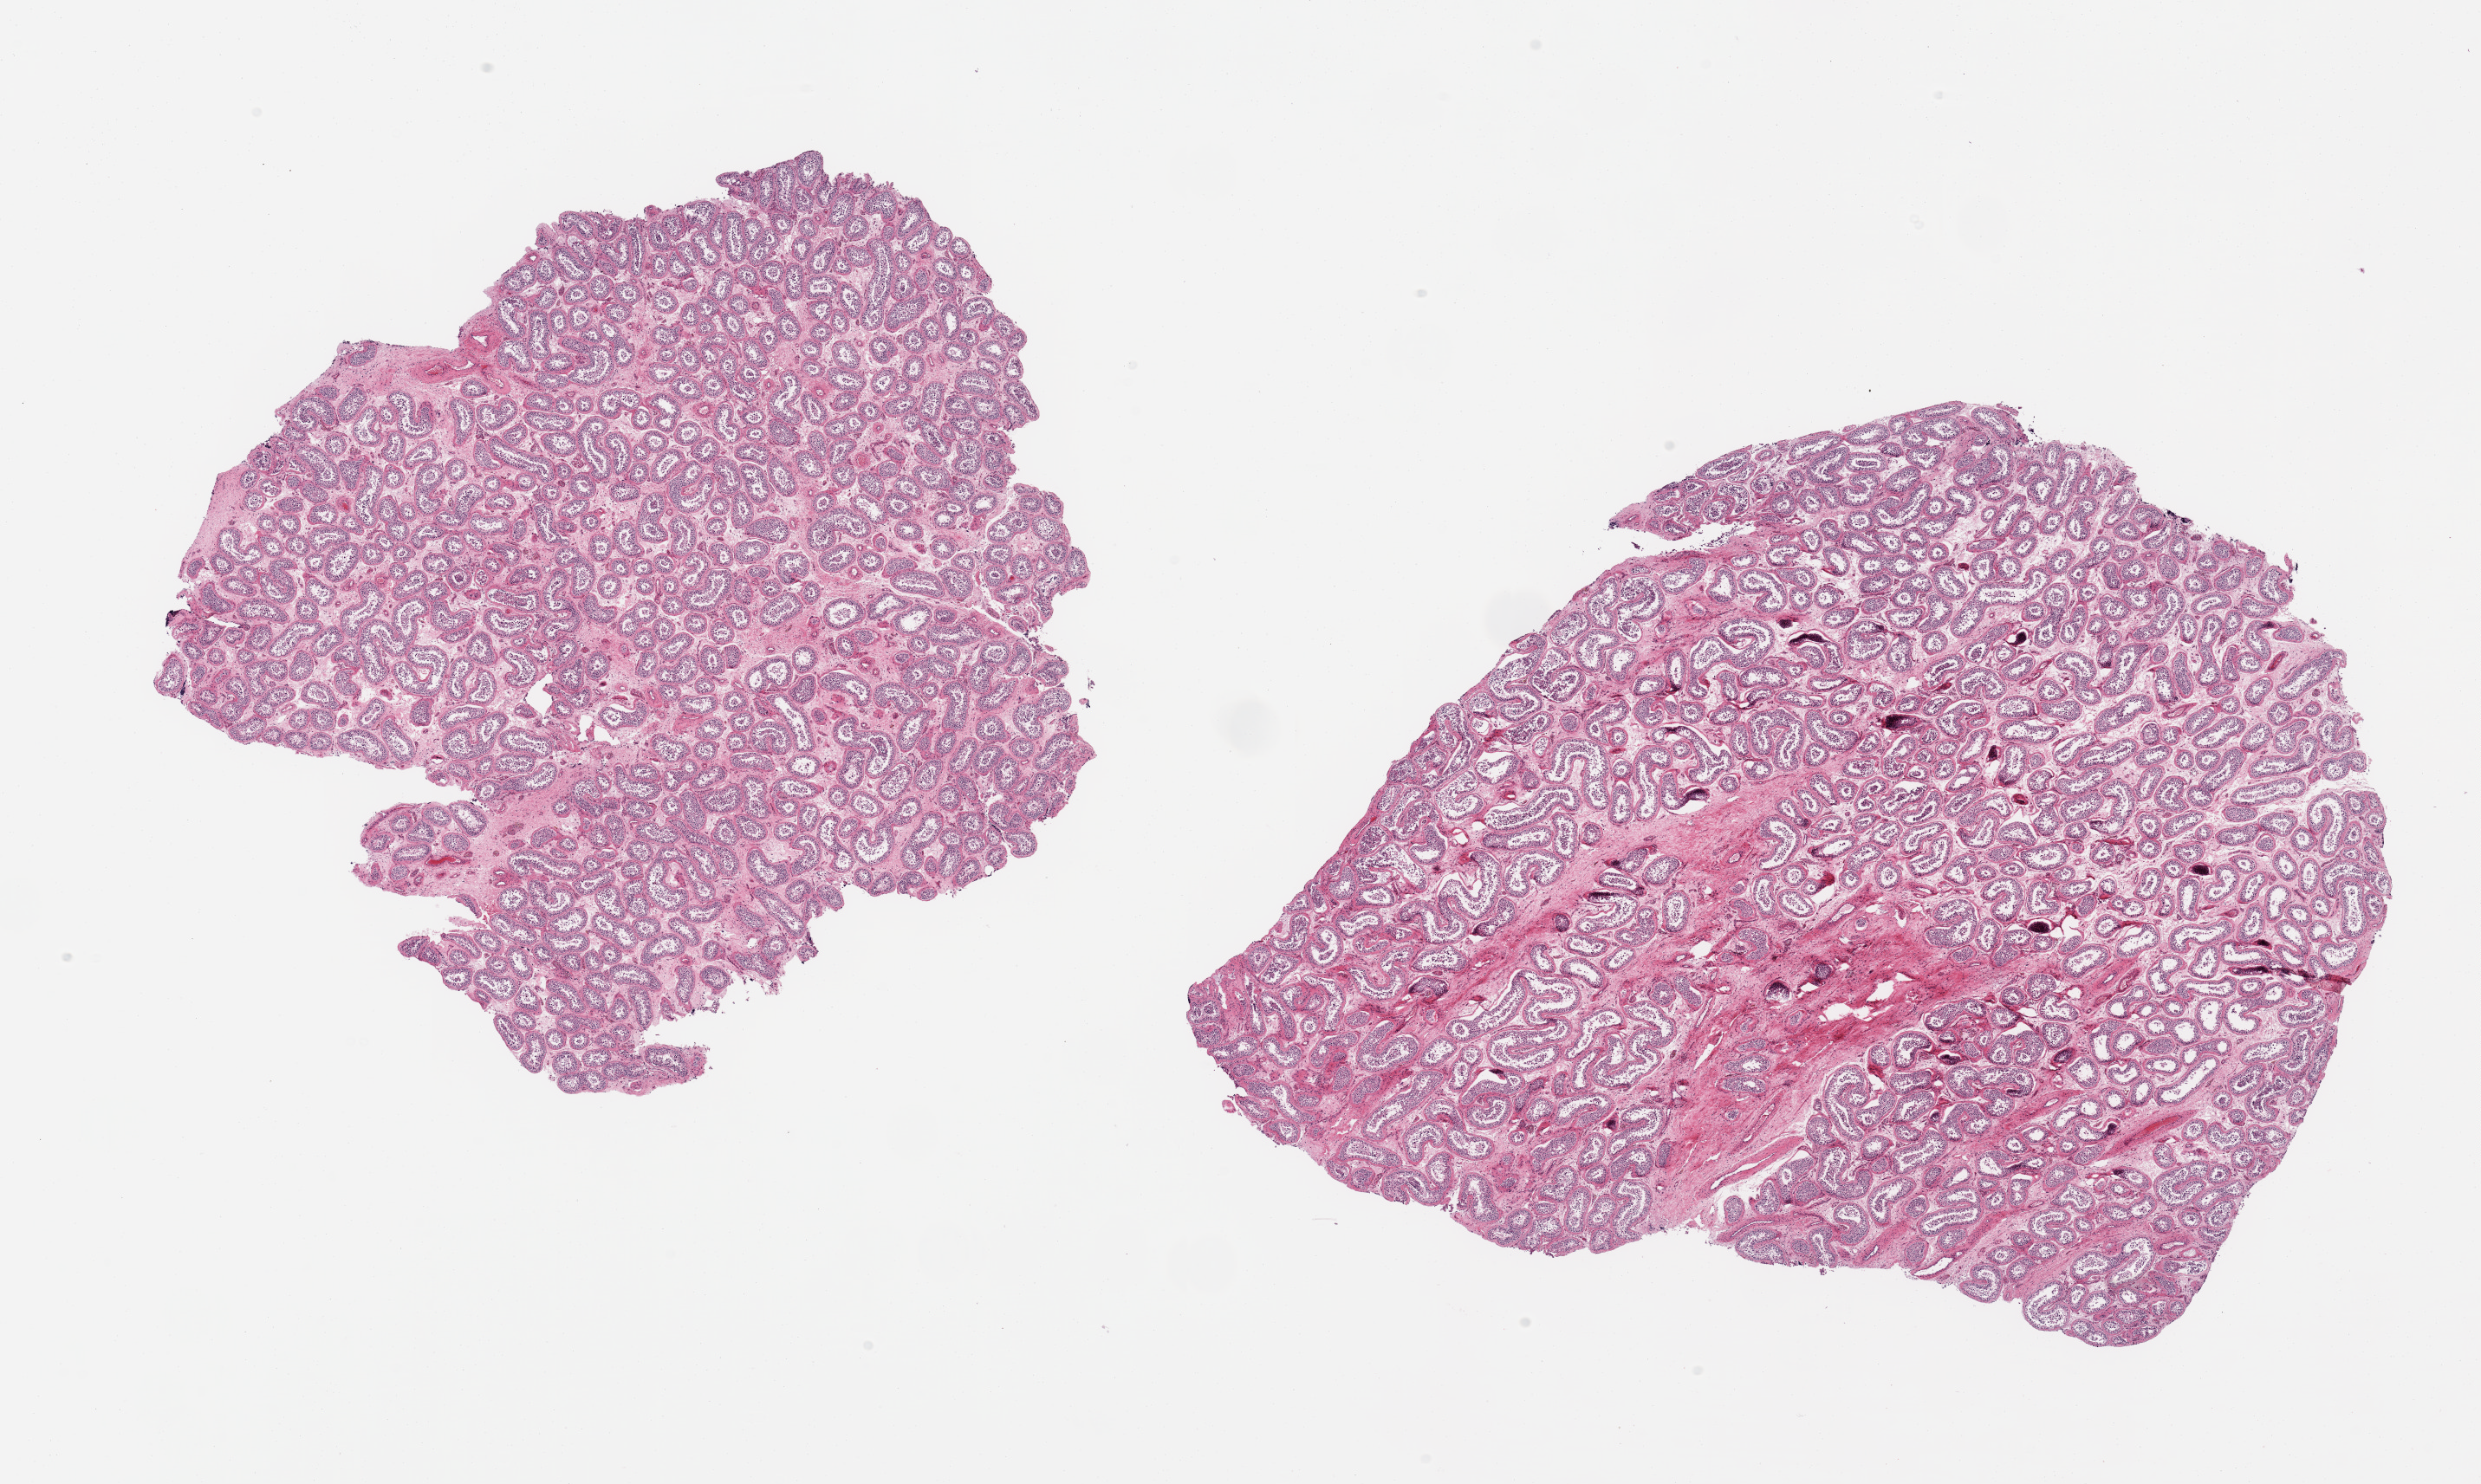
Whole-slide image, hematoxylin and eosin (H&E) stain, whole scanned area (about 22.6 x 13.5 mm, acquisition: 20x scan) shown as a low-resolution overview. PAXgene-fixed, paraffin-embedded tissue. Sampled site (target tissue): testis. Tissue donor sample. Male donor.
Review note (as recorded): 2 pieces, spermatogenesis present, appears reduced.